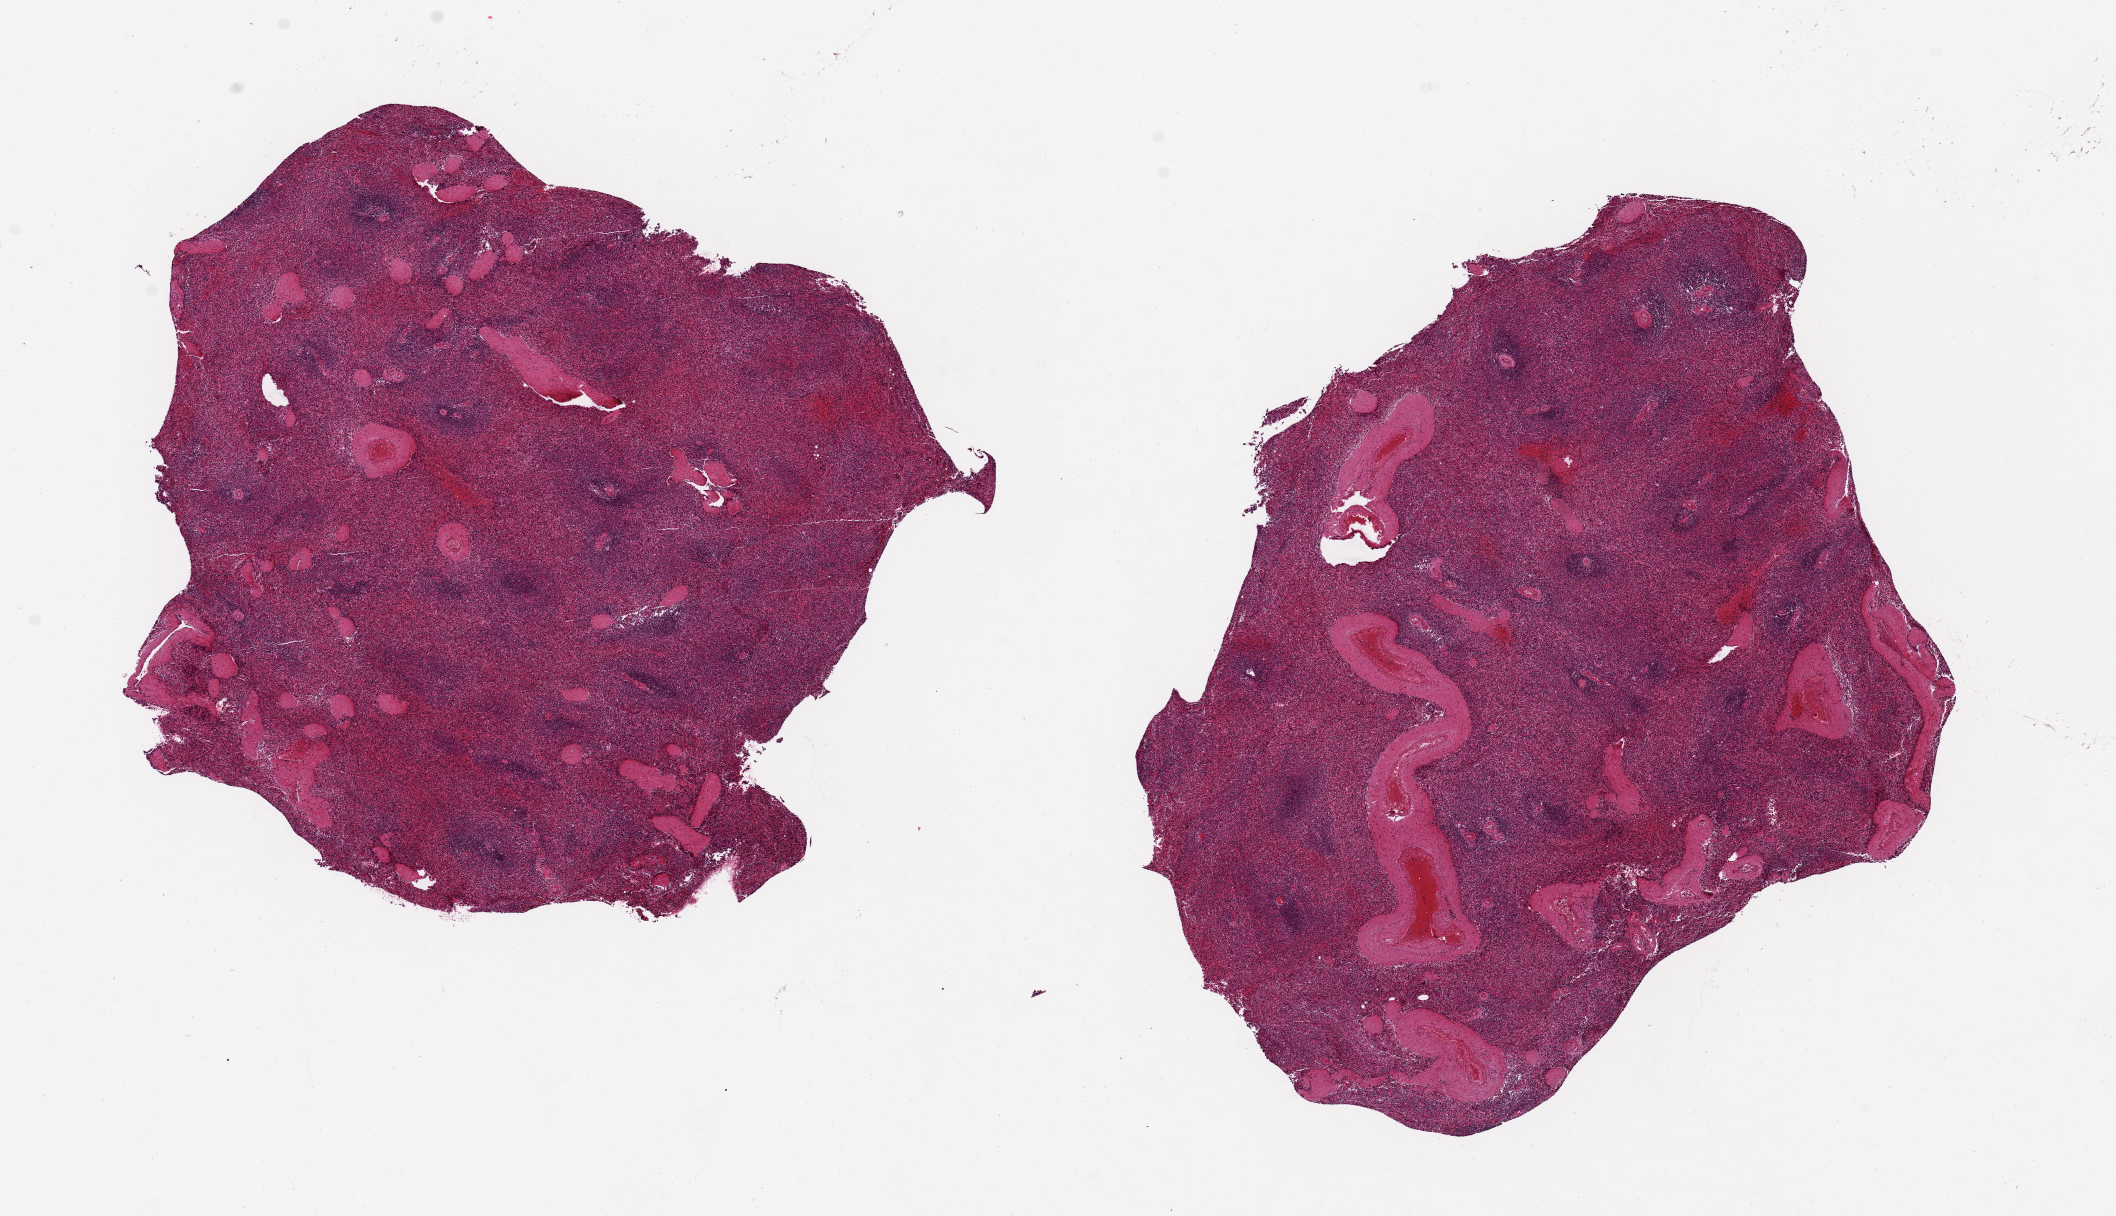
Whole-slide image, hematoxylin and eosin (H&E) stain, brightfield — a low-resolution overview of the entire scanned area, about 16.7 x 9.6 mm (from a 20x scan), PAXgene-fixed, paraffin-embedded tissue, sampled site (target tissue): spleen, donor tissue sample. Male donor.
* review note (as recorded): 2 aliquots, ~6.5x6mm. Marked congestion